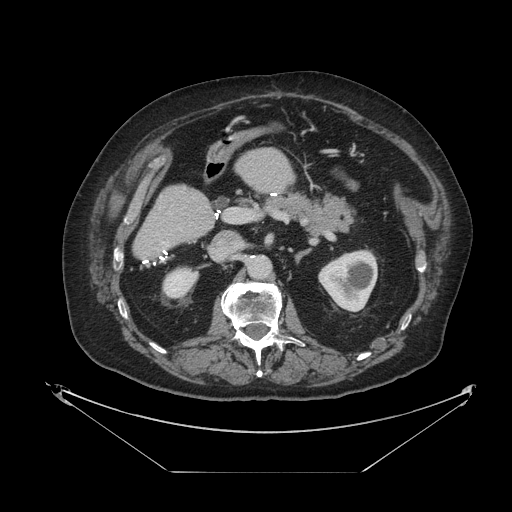
Contrast-enhanced abdominal CT, one axial slice. Position 45 of 121 along the scan axis. Soft-tissue window (W 400 / L 40 HU). 2.5 mm slice thickness. 512 × 512 image matrix, field of view 500 × 500 mm. Male patient, age 68 years. Case-level facts recorded for this patient, not image findings: diagnosis: colorectal cancer liver metastases, imaged before liver resection; multiple liver metastases: no; largest metastasis: 4 cm; disease in both lobes: no.
Annotated regions visible in this slice (expert manual segmentation):
- liver: box from (x=134, y=149) to (x=294, y=260) px
- planned liver remnant (the part of the liver to remain after resection): (x=134, y=149)–(x=294, y=260)
- portal vein (with intrahepatic branches): (x=226, y=209)–(x=236, y=221)